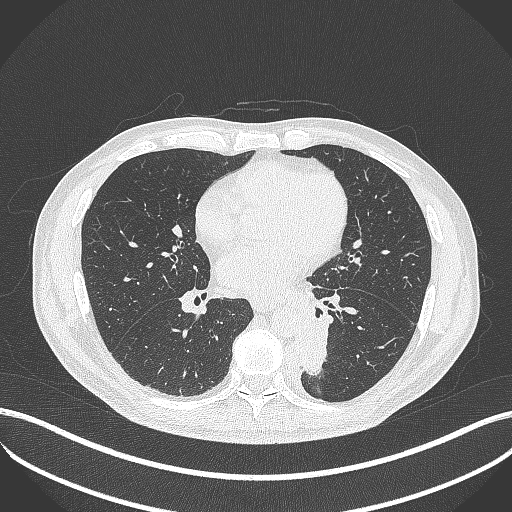
Chest CT, one axial slice; position 188 of 451 along the scan axis; reconstruction kernel B70f; 120 kVp; lung window (W 1500 / L -600 HU); 1 mm slice thickness; 512 × 512 image matrix, field of view 400 × 400 mm. Male patient, age 72 years. From the clinical record (not read from this slice): clinical TNM (as recorded): T2b N0 M1.
Structures marked on this image (bounding box drawn by a radiologist):
- lung tumour (recorded histology: adenocarcinoma): box from (x=298, y=316) to (x=333, y=377) px